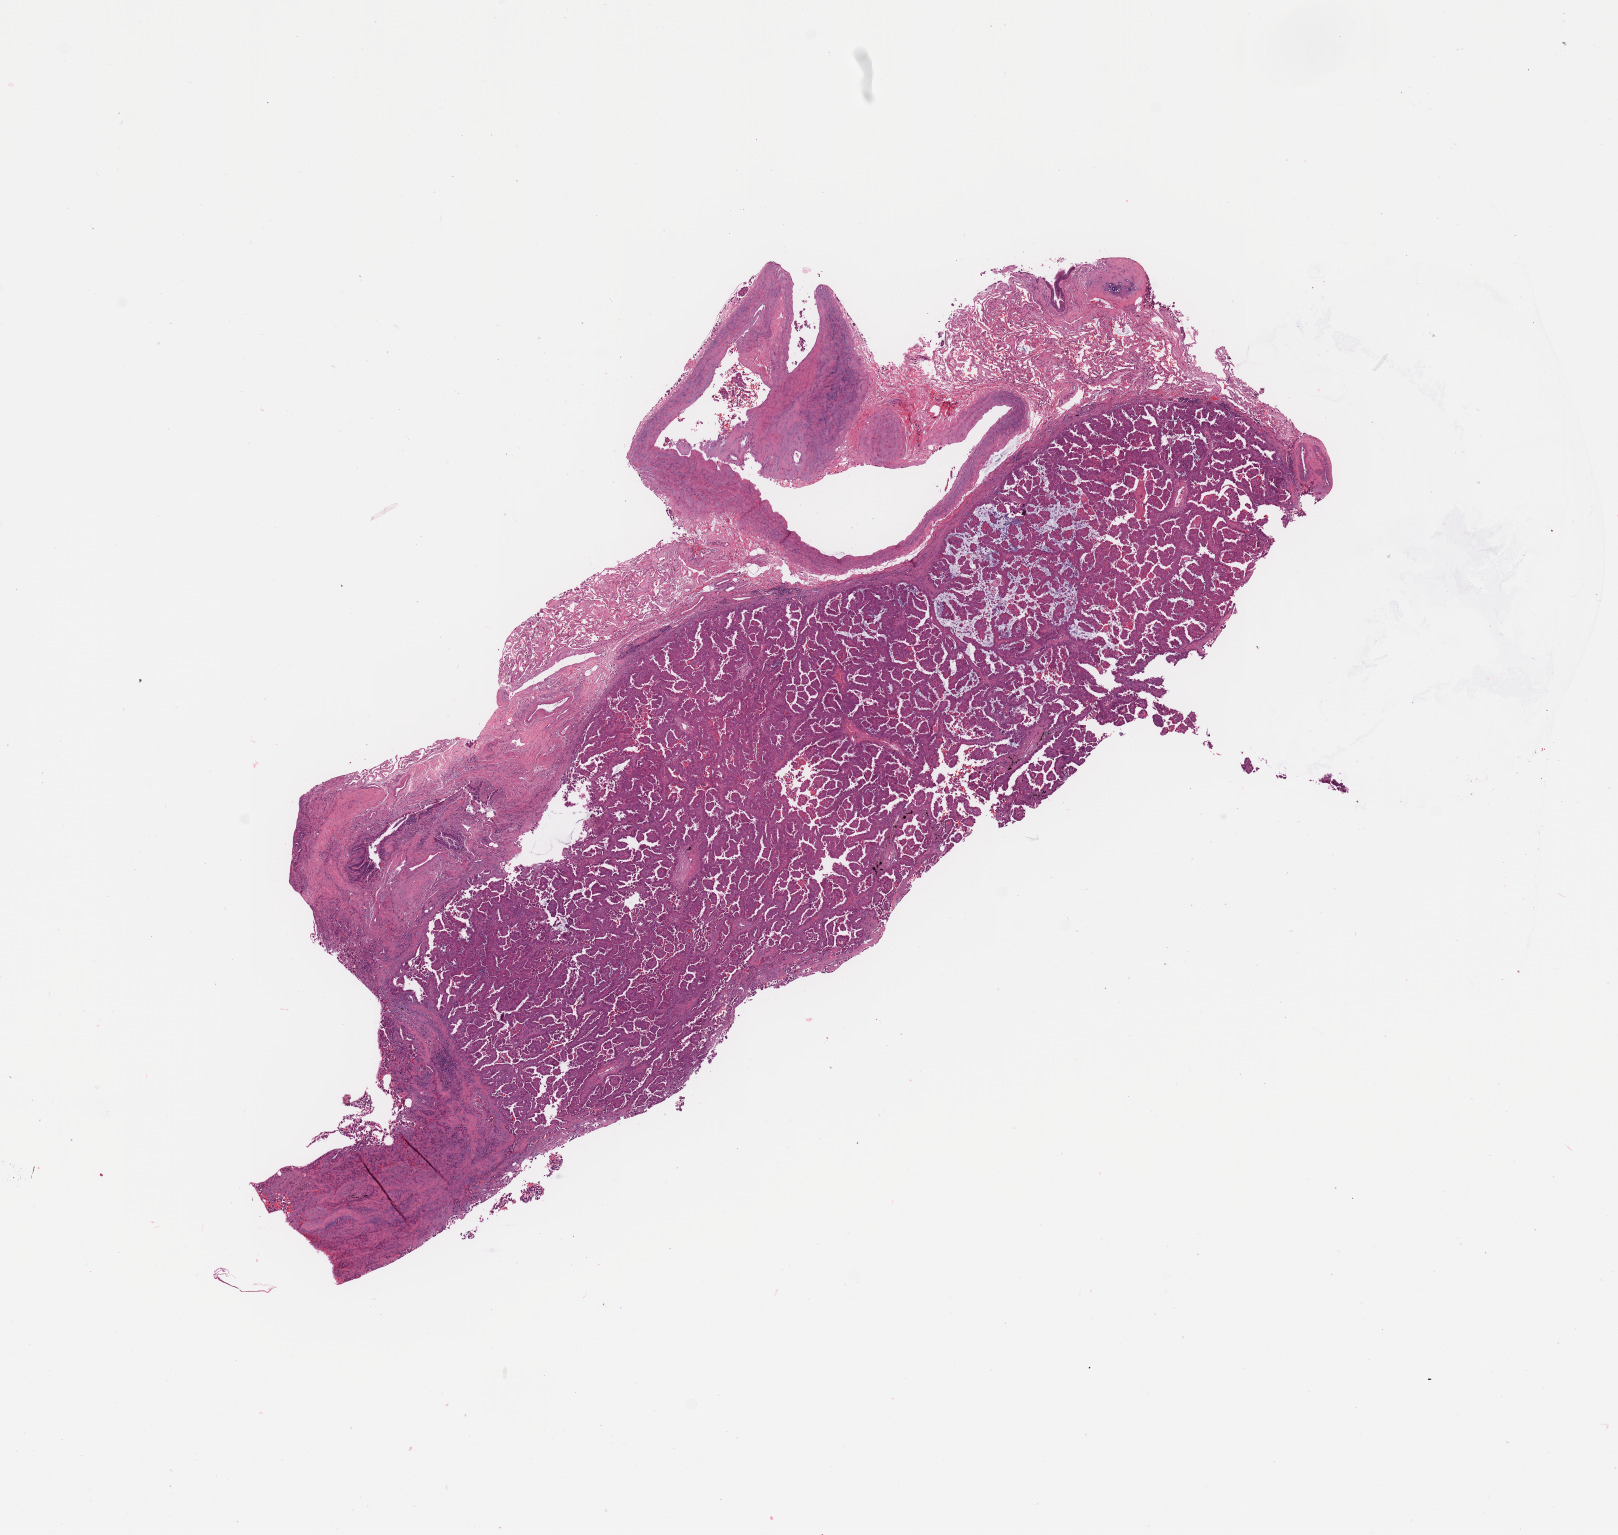
Digitized Hematoxylin and eosin (H&E) stained tissue section (whole slide) — shown as a low-resolution overview of the whole scanned area (about 12.8 x 12.1 mm, from a 20x scan). Tumour tissue sample, lung. 77-year-old male patient. Histologic grade: G2 (moderately differentiated).
Diagnosis: Adenocarcinoma, NOS. AJCC pathologic stage: IIA.